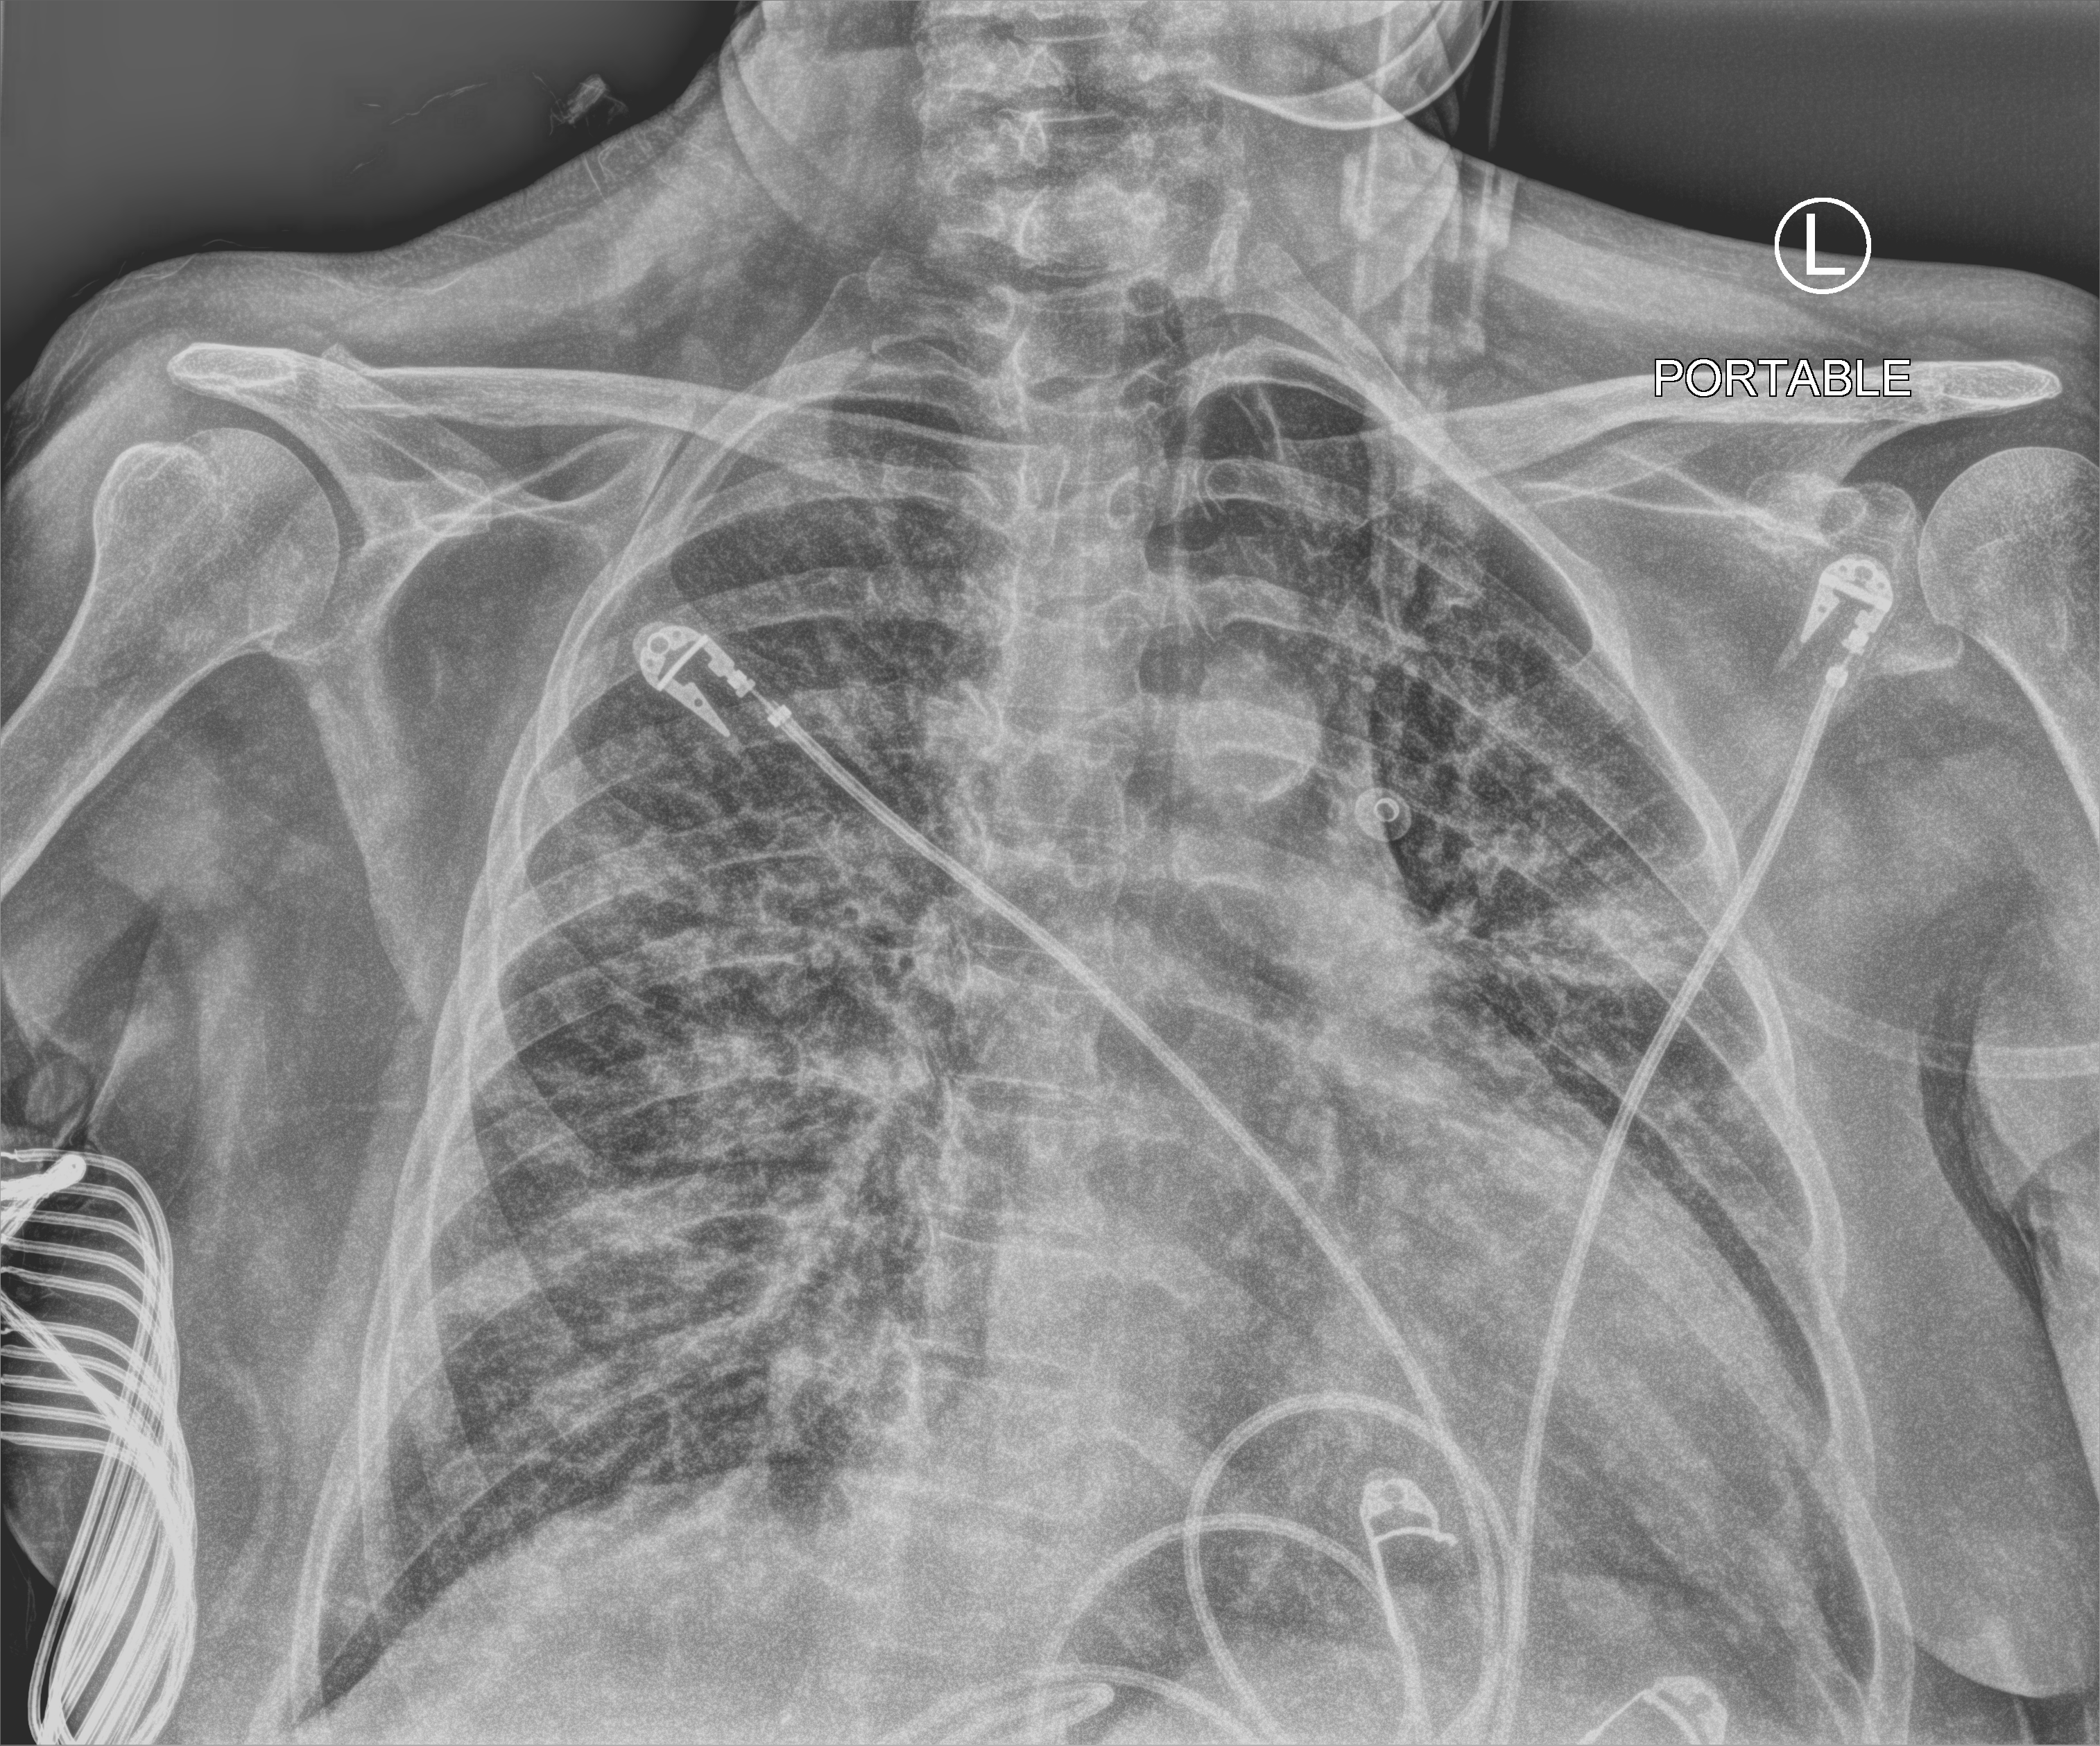
Chest X-ray (portable). Patient hospitalised with COVID-19; female, aged 60–74 years.
From the hospital-stay record, not from the radiograph (when in the stay this image was taken is not recorded):
- admitted to intensive care during this hospital stay: yes
- mechanically ventilated during this hospital stay: no